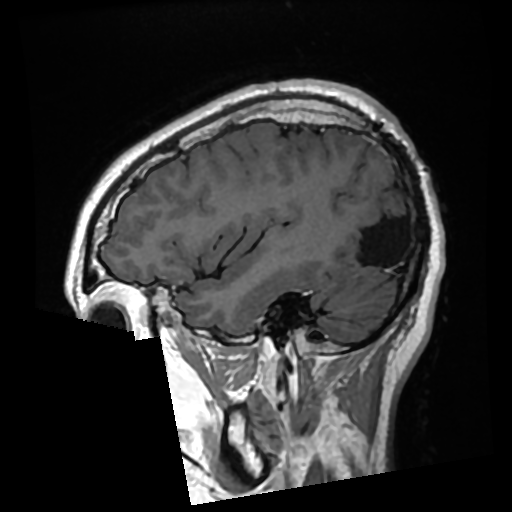
Brain MRI from a brain-tumour surgery series, one sagittal slice. Slice 83 of 276 in the series (ordered by position). T1-weighted post-contrast. 0.7 mm slice thickness. 512 × 512 image matrix, field of view 250 × 250 mm. From the clinical record (not read from this slice): histopathology: Glioma with ependymal features; WHO grade: 2; tumour location: Left Parietal.
Structures marked on this image (expert manual segmentation):
- previous resection cavity: bounding box [x1, y1, x2, y2] px = [344, 184, 404, 266]